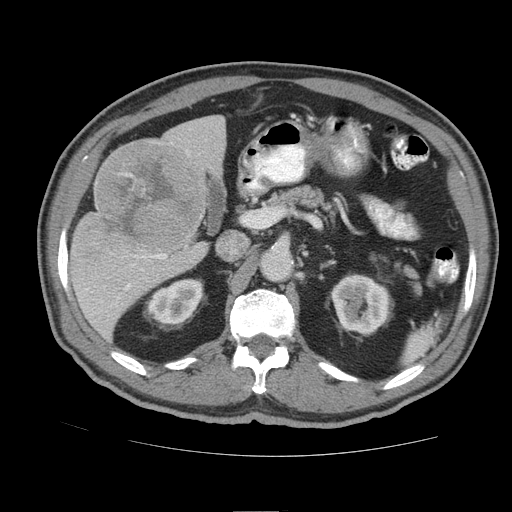
Contrast-enhanced abdominal CT (liver protocol), one axial slice. Slice 47 of 105 in the series (ordered by position). 140 kVp. Soft-tissue window (W 400 / L 40 HU). 2.5 mm slice thickness. 512 × 512 image matrix. Case-level facts recorded for this patient, not image findings: diagnosis: hepatocellular carcinoma (patient treated with transarterial chemoembolisation; whether this scan precedes or follows treatment is not stated here); TNM stage (as recorded): Stage-IIIB; Child-Pugh class: A; tumour nodularity: multinodular.
Outlined on this slice (semi-automatic segmentation, software-assisted and operator-edited):
- liver parenchyma outside the tumour (the mass and vessels are separate outlines, so this box may not span the whole liver): bounding box (x1, y1, x2, y2) in pixels: (68, 116, 226, 340)
- mass: (72, 141, 201, 257)
- liver vessels: (87, 254, 167, 299)